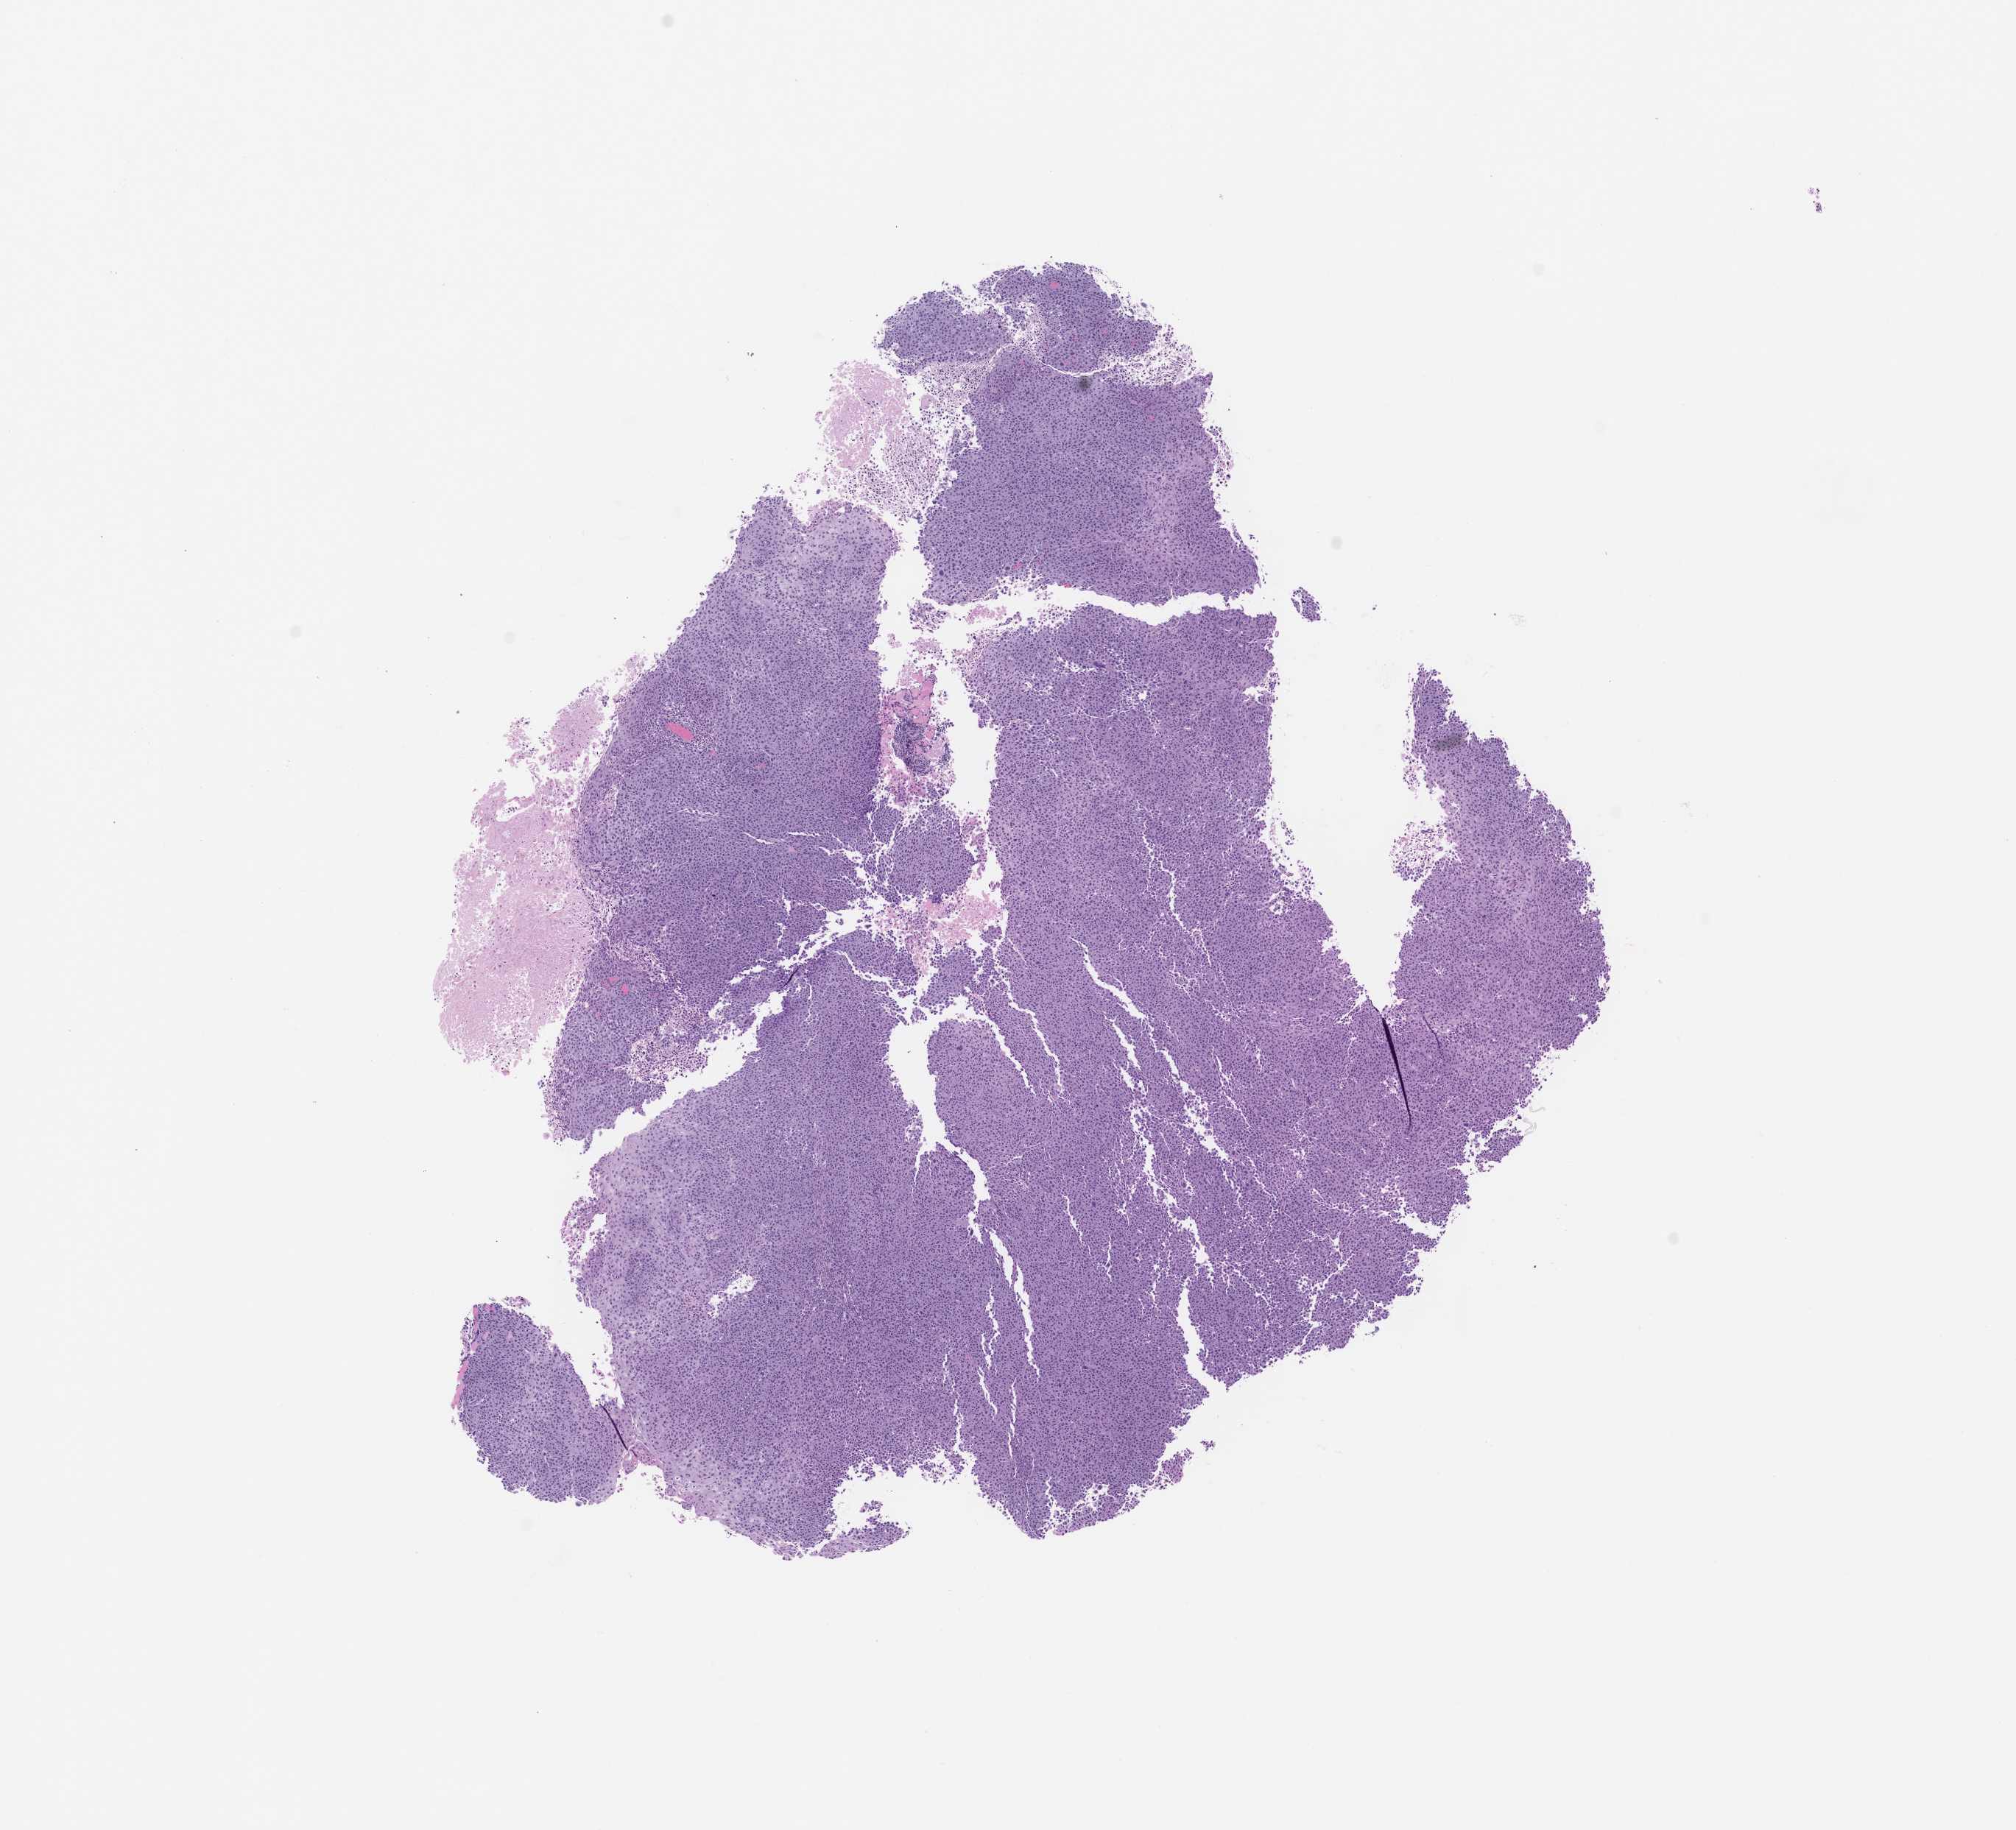
Hematoxylin and eosin (H&E) whole-slide image of a patient-derived xenograft (PDX) tumor grown in a mouse, passage 1 — a low-resolution overview of the entire scanned area, about 11.0 x 10.0 mm. FFPE section. Tumor site category: head and neck.
Originating patient diagnosis: Head and Neck Squamous Cell Carcinoma.